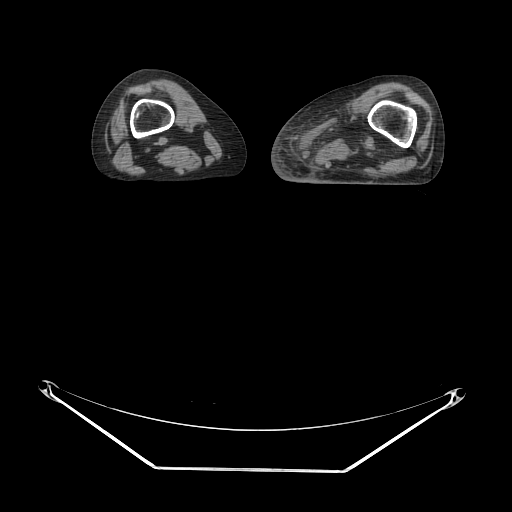
CT of an extremity soft-tissue mass (from a PET/CT study), one axial slice. Position 1 of 91 along the scan axis. 140 kVp. Soft-tissue window (W 400 / L 40 HU). 512 × 512 image matrix, field of view 500 × 500 mm. Female patient. From the clinical record (not read from this slice): histological type: pleomorphic leiomyosarcoma; grade: high; site of the primary tumour: left thigh.
Structures marked on this image (expert contour drawn on MRI and transferred to this co-registered scan by the dataset authors):
- gross tumour volume including surrounding oedema: bounding box (x1, y1, x2, y2) in pixels: (308, 103, 375, 170)